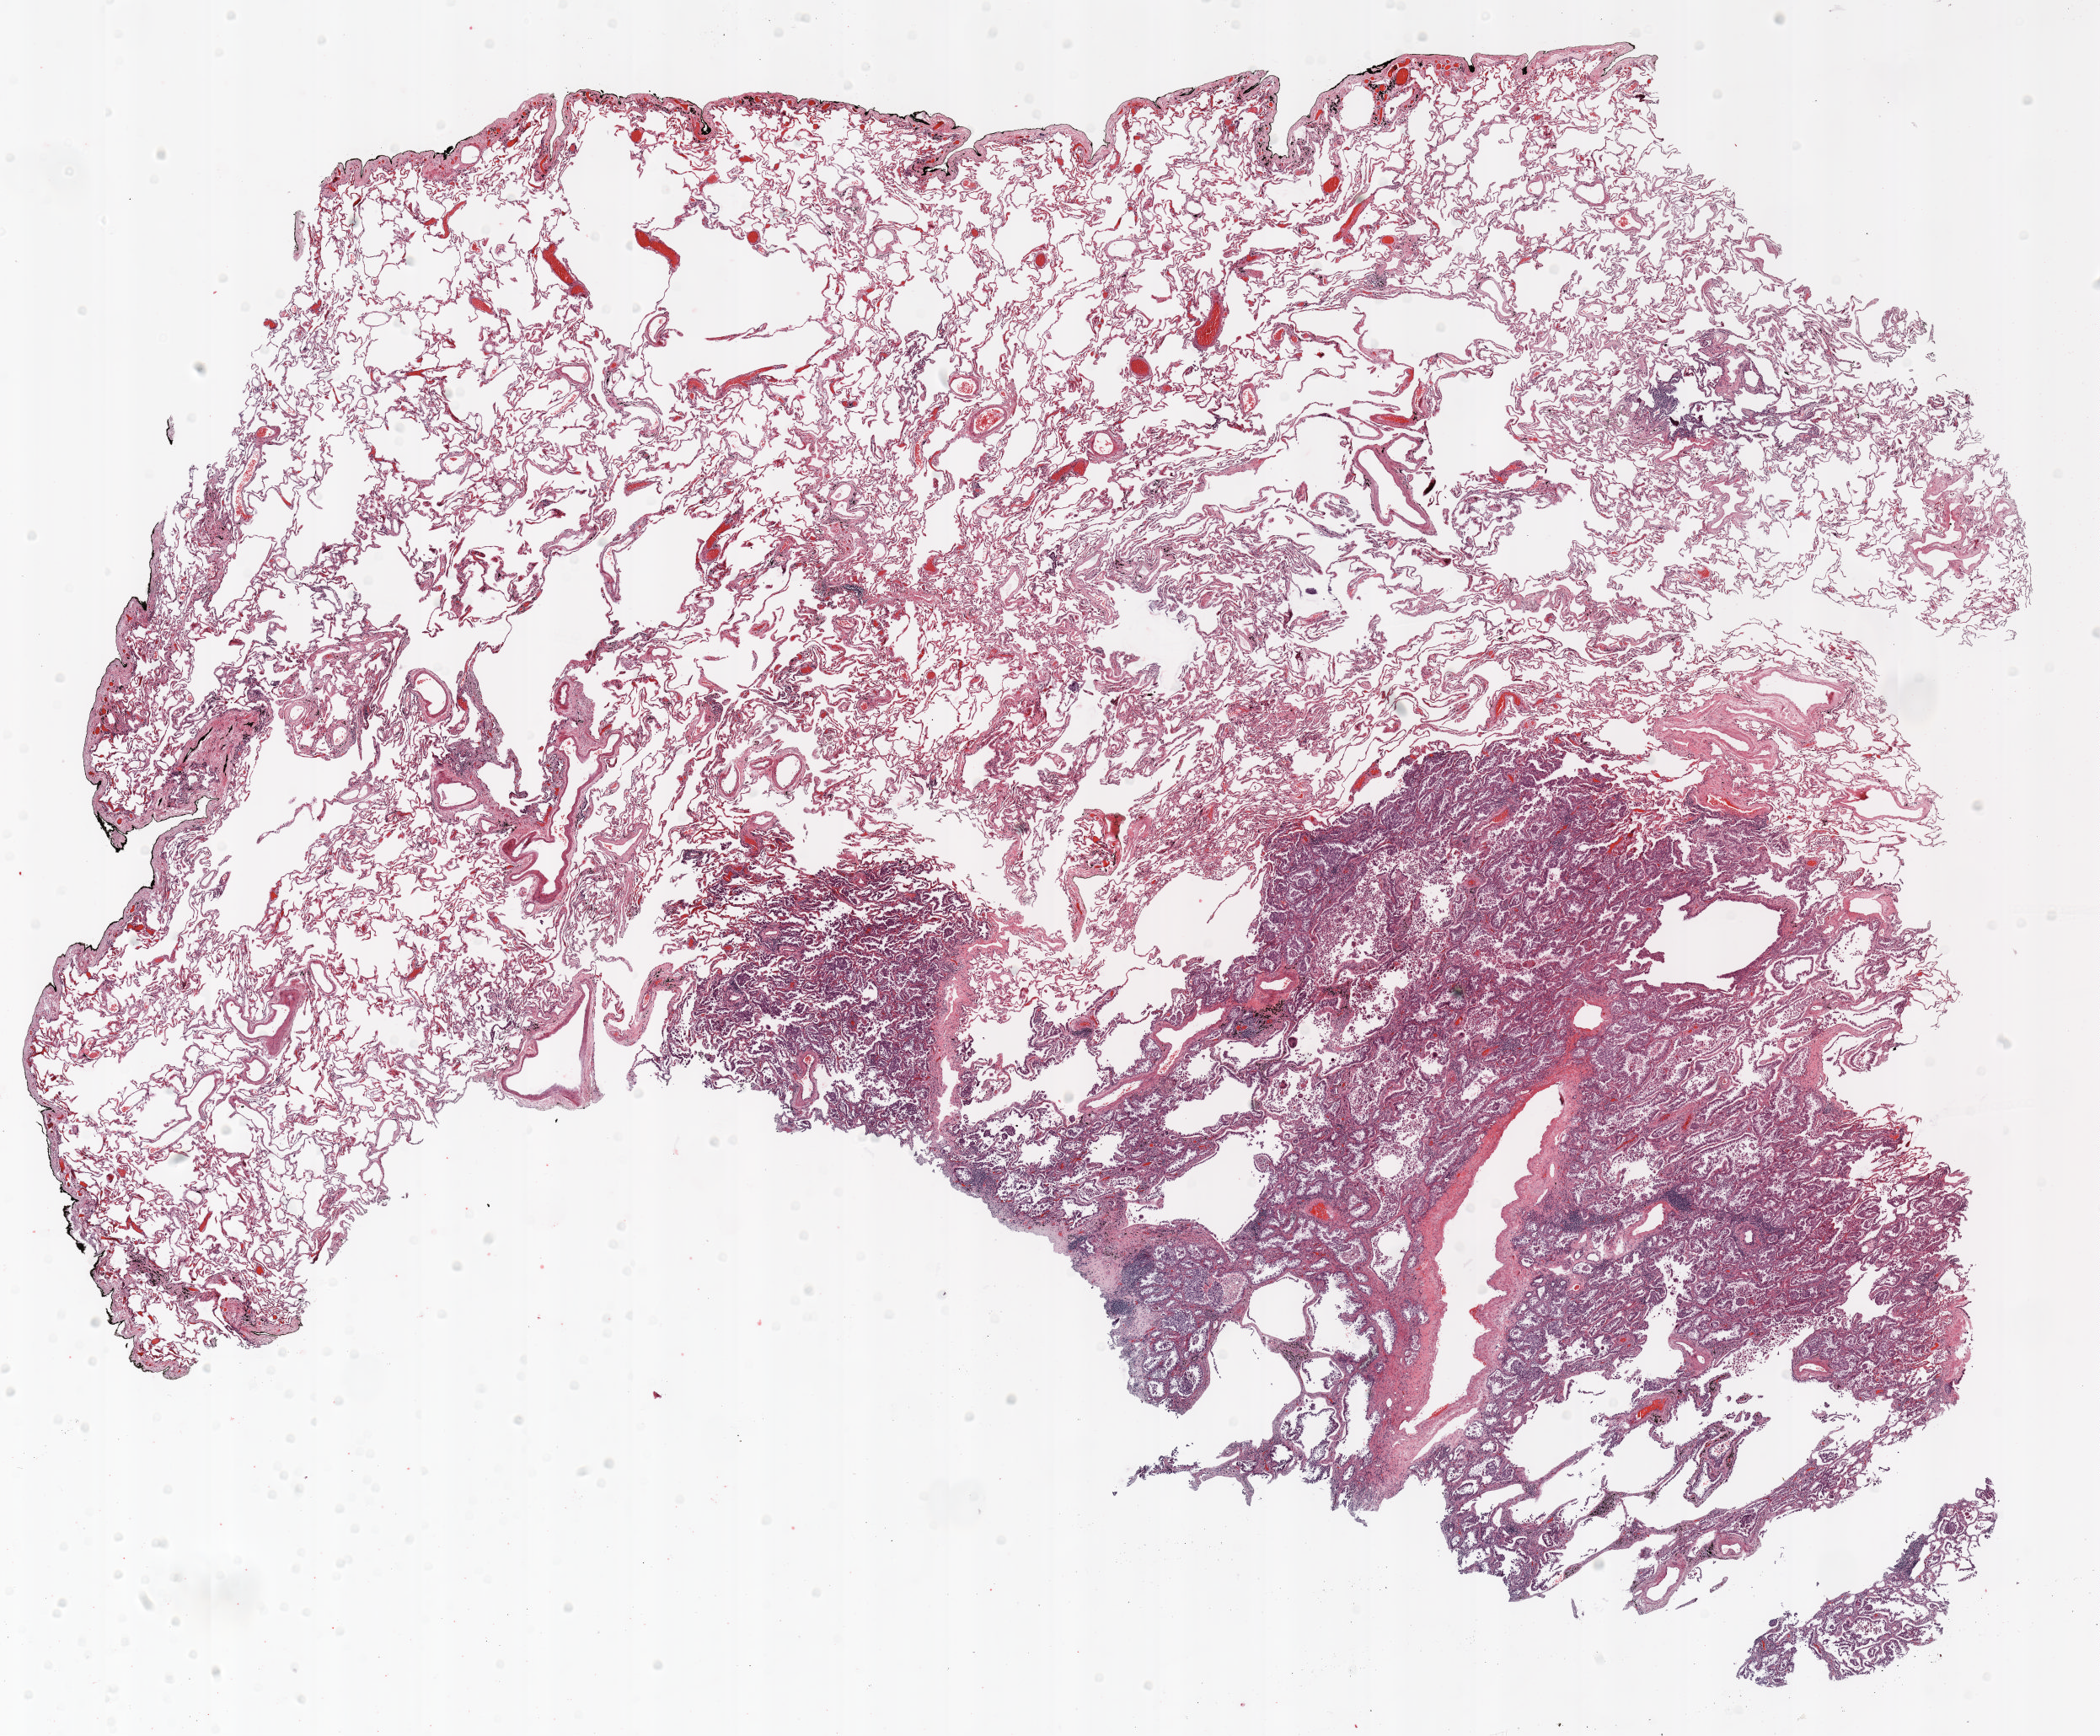
H&E whole-slide image — whole scanned area (about 20.0 x 16.5 mm) shown as a low-resolution overview. Formalin-fixed paraffin-embedded (FFPE) section. Lung tissue. Male patient, aged 68 at enrolment. Grade: moderately differentiated (G2).
Stage (AJCC 6th edition): IA. Primary tumour location (clinical record): right upper lobe. Tumour size (pathology): 28 mm. Participant's lung-cancer diagnosis: Adenocarcinoma, NOS.